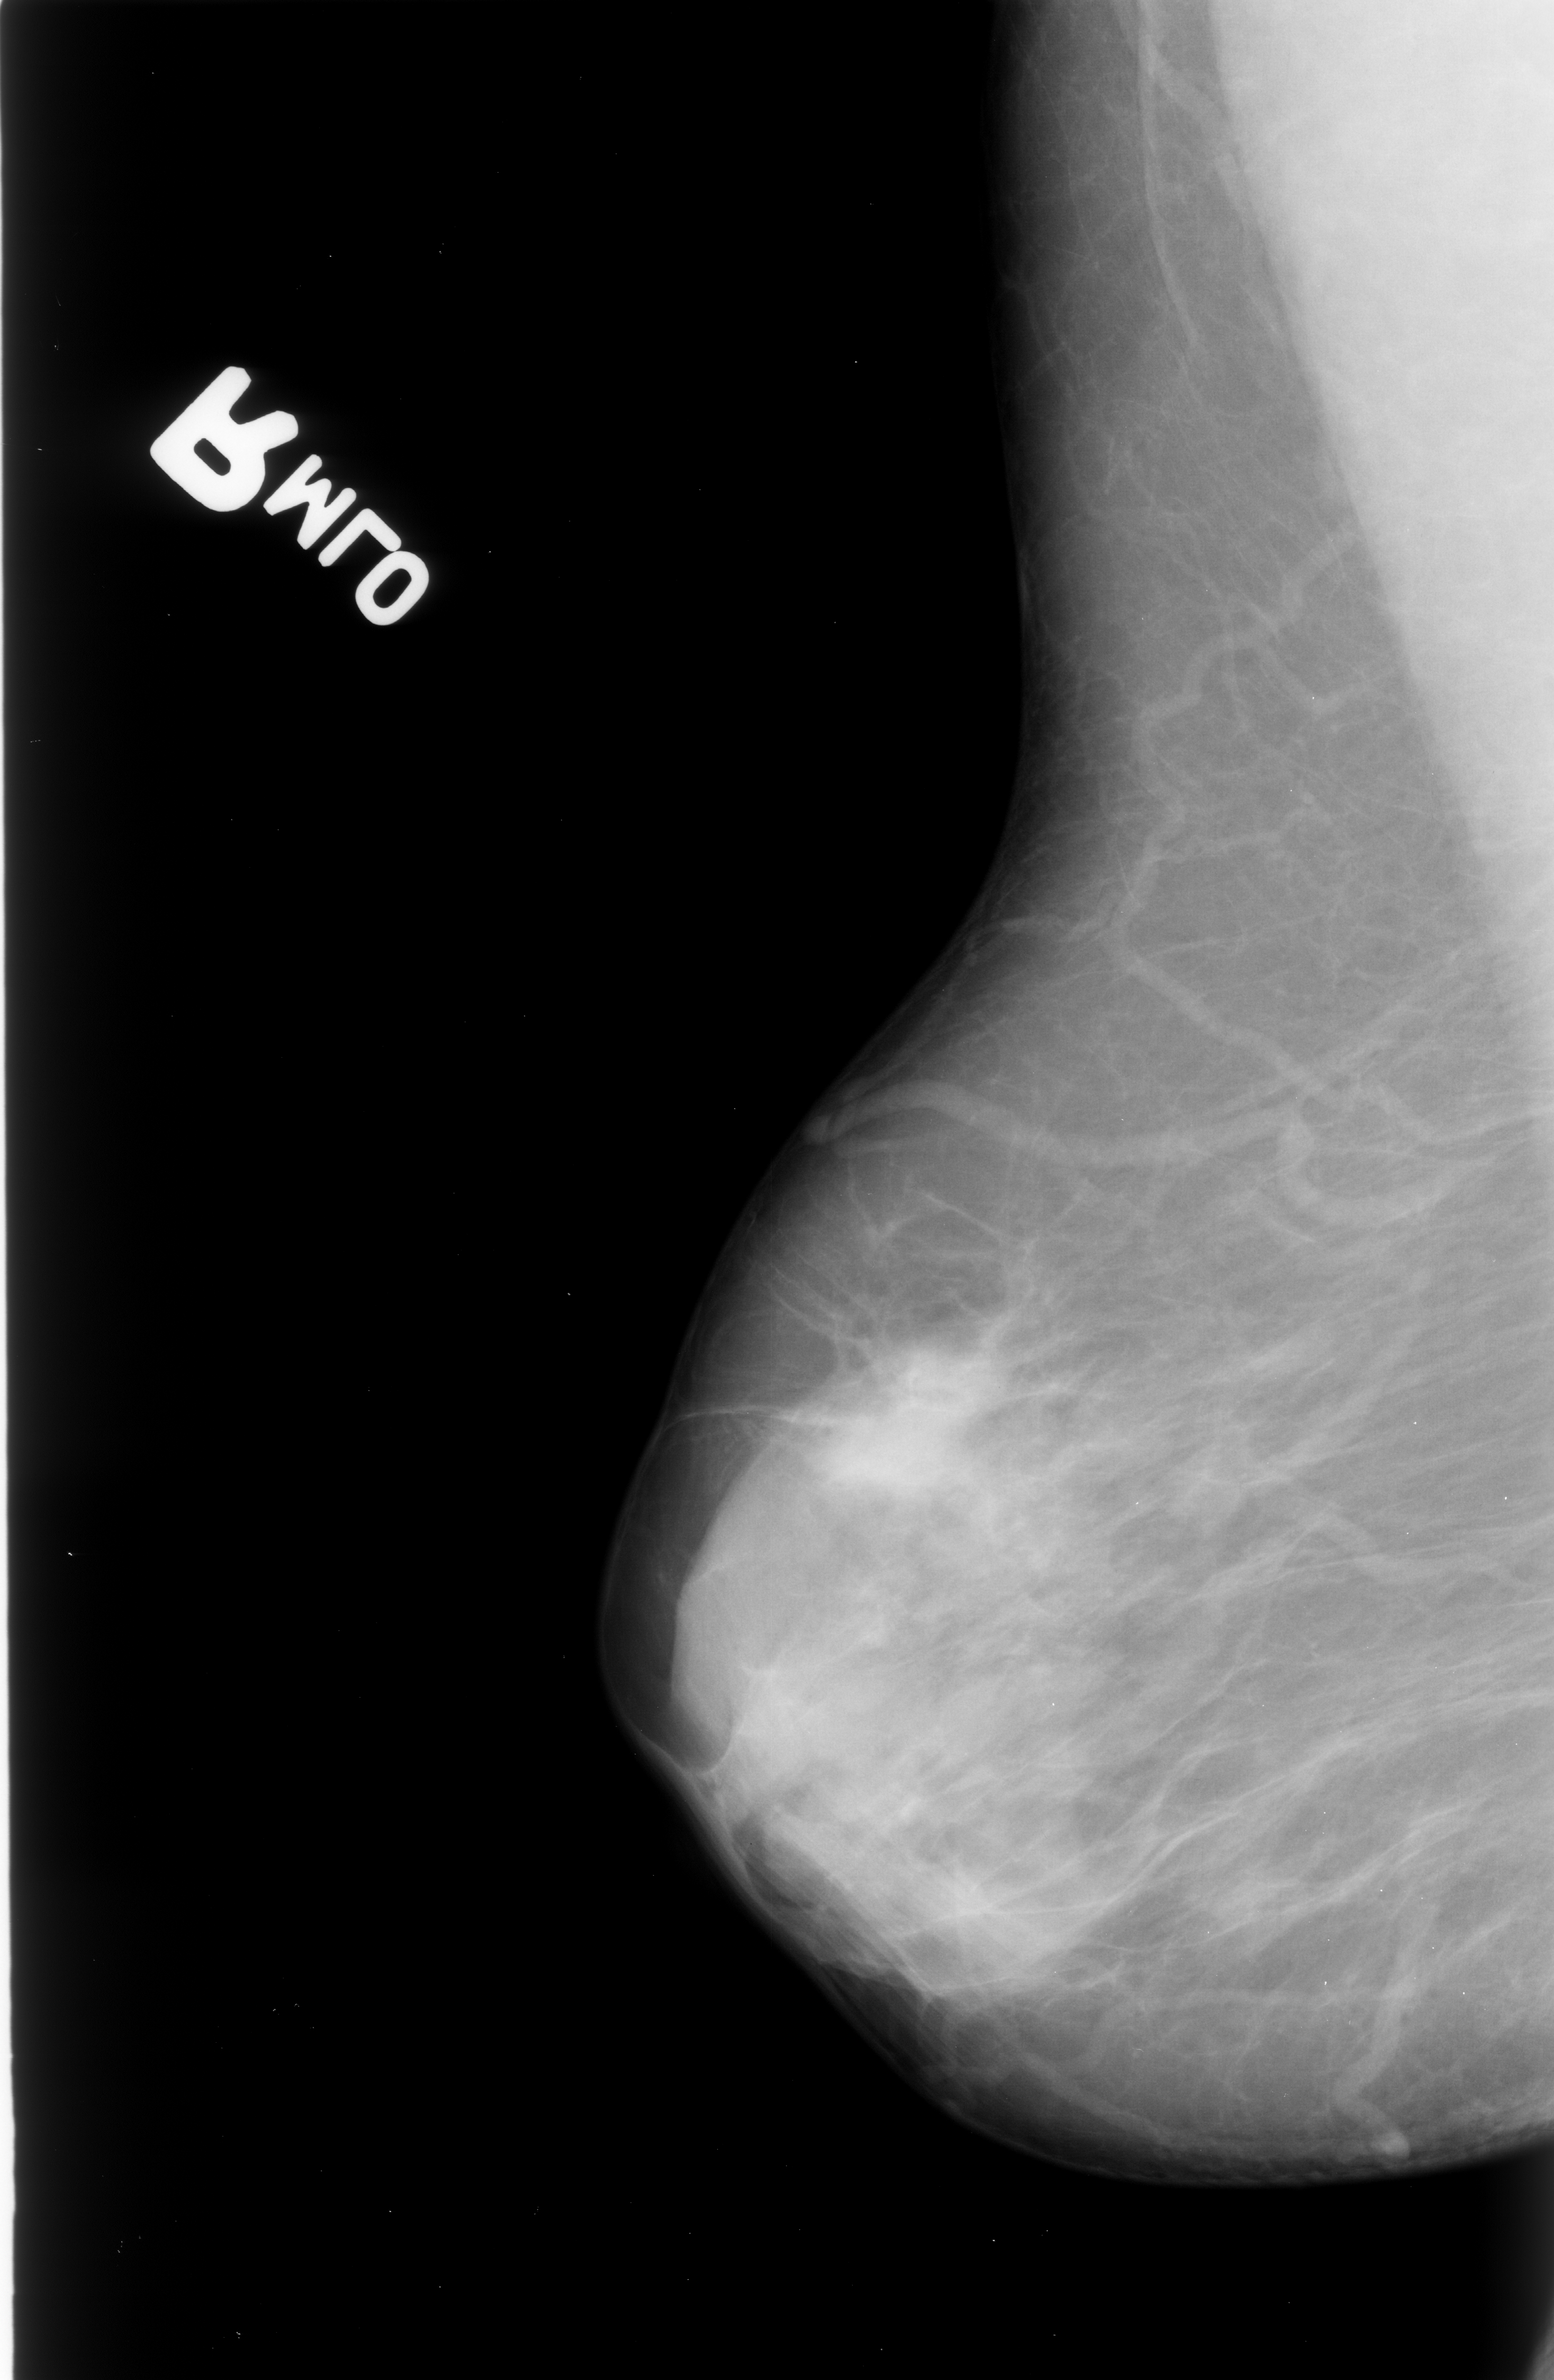
Mammogram (digitized film), right breast, MLO view.
- Marked abnormality: mass, shape irregular / architectural distortion, margins obscured / spiculated; BI-RADS assessment category 4; subtlety rating 3 on a 1 (subtle) to 5 (obvious) scale; pathology (as recorded): malignant.